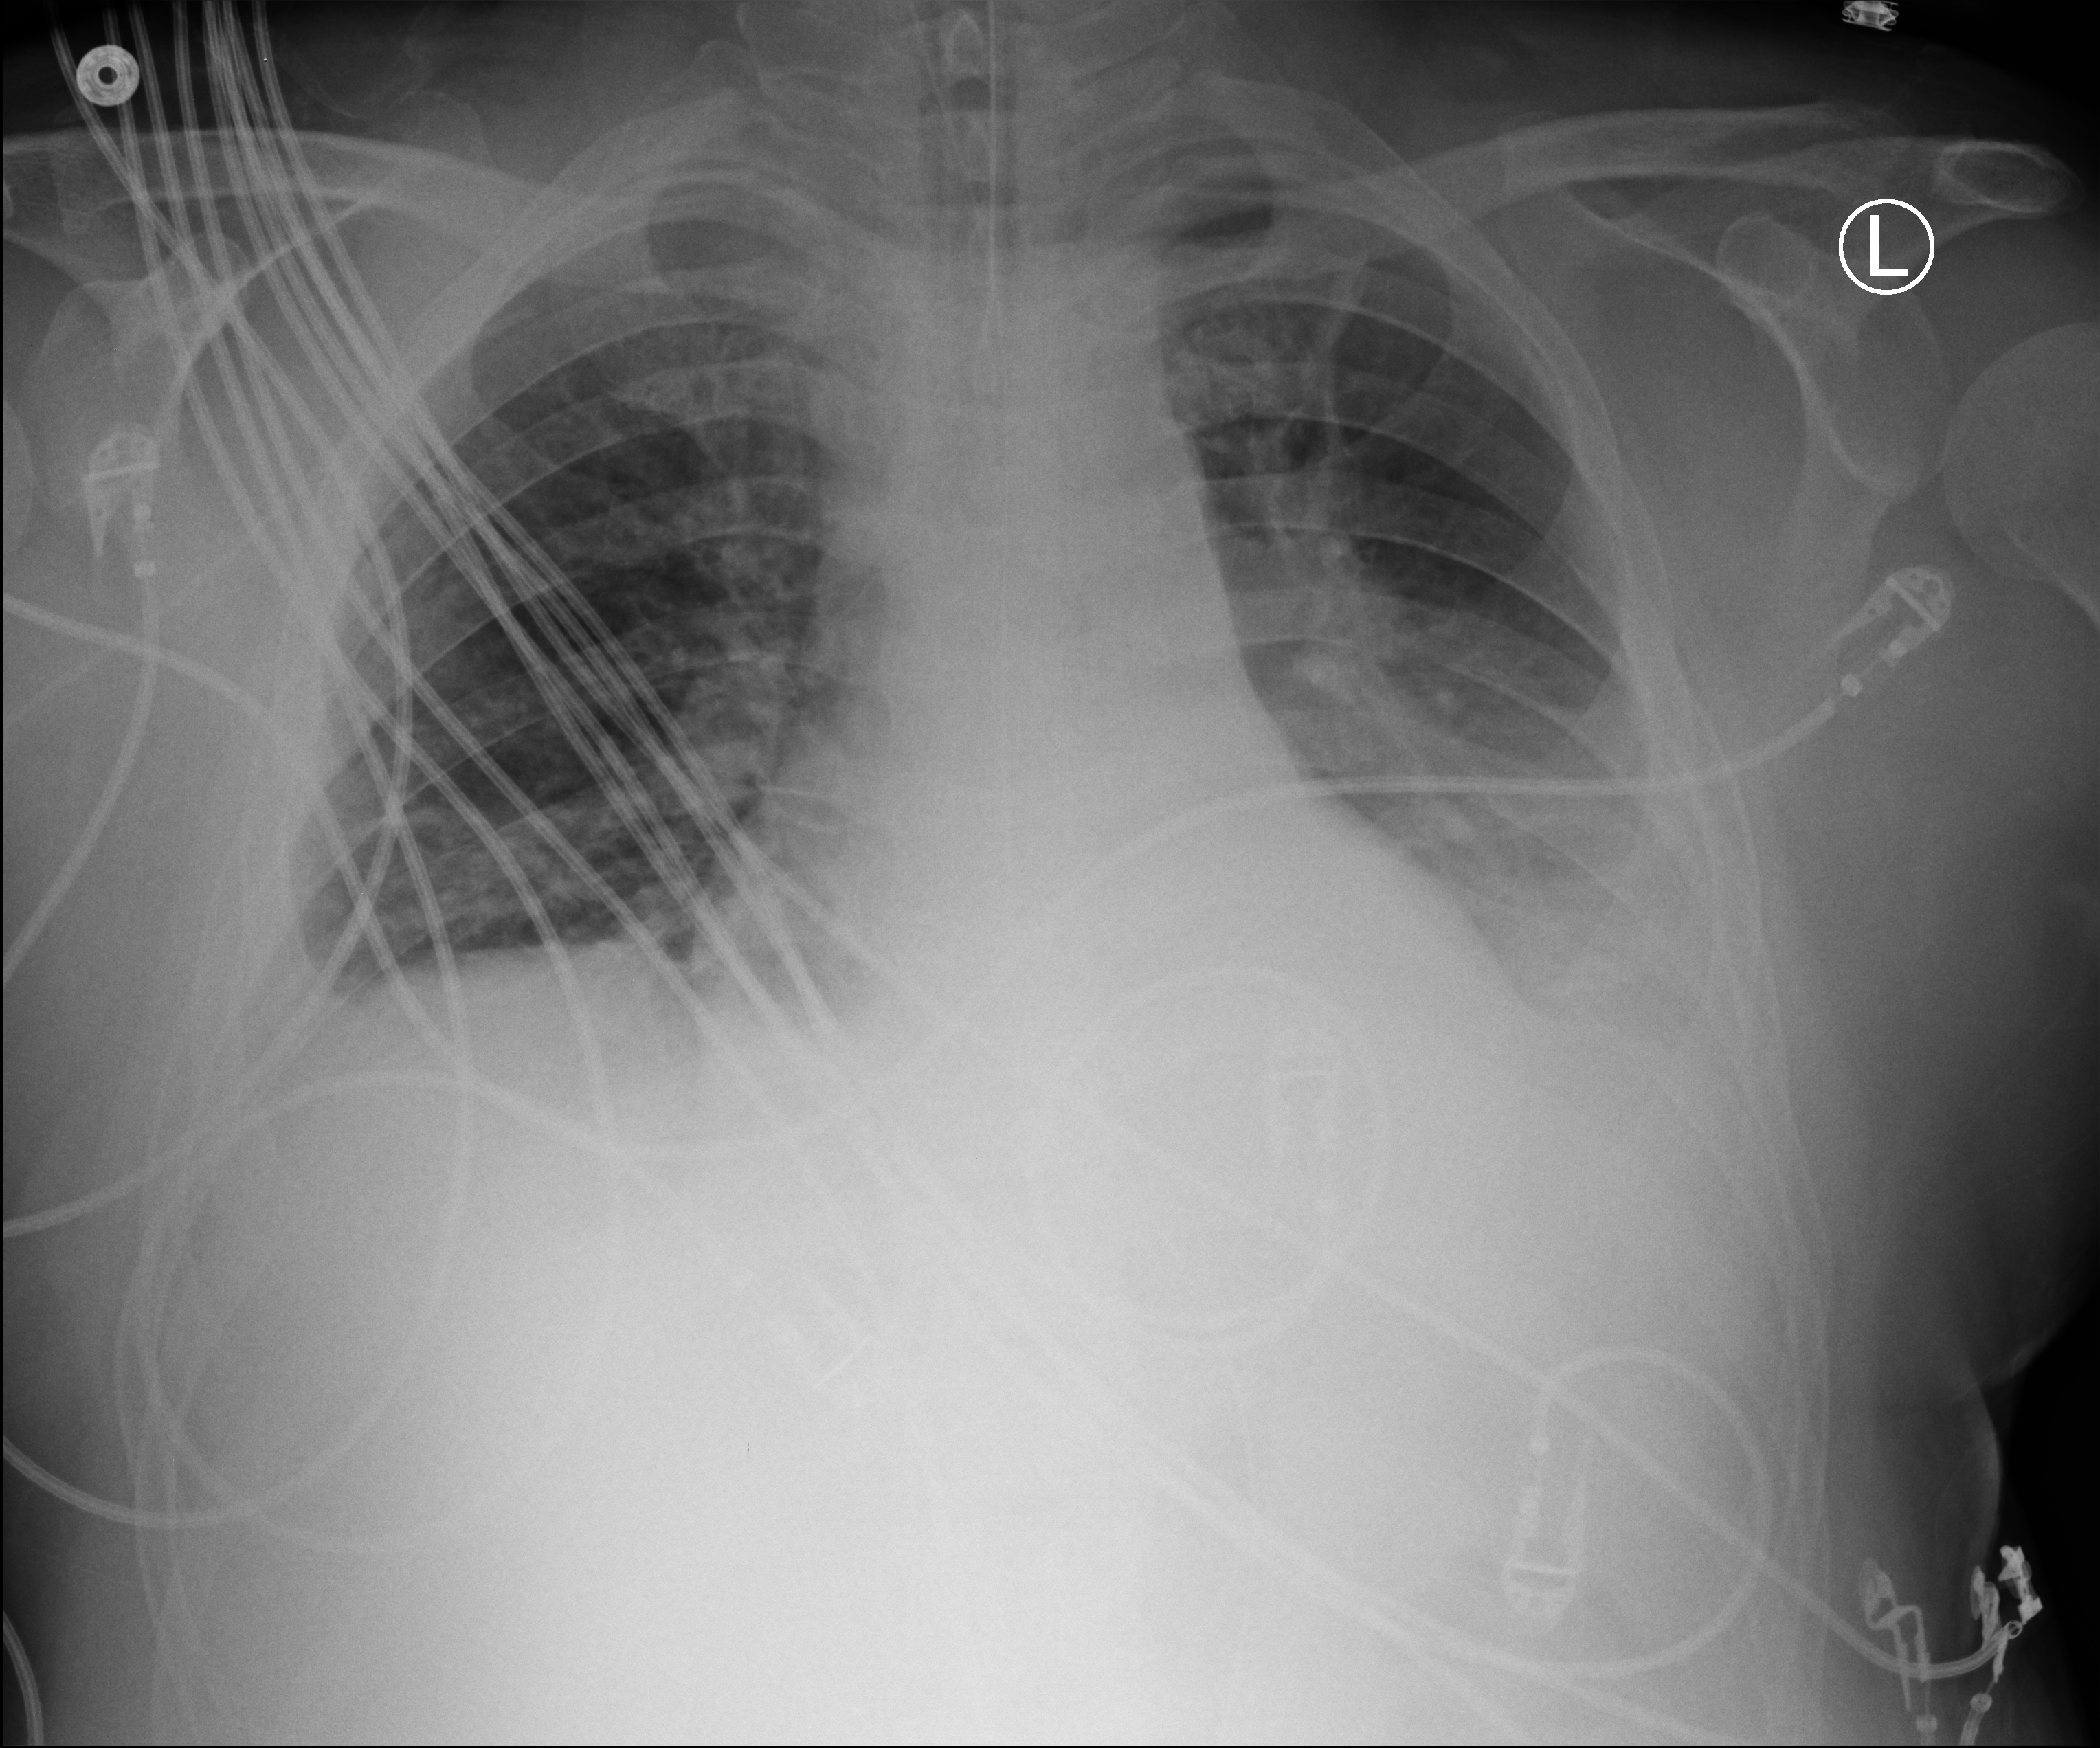
Chest X-ray (portable); anteroposterior (AP) projection. Patient hospitalised with COVID-19; male, aged 18–59 years.
Hospital-stay facts (about this admission, not read from this image; timing relative to this image not recorded):
- admitted to intensive care during this hospital stay: yes